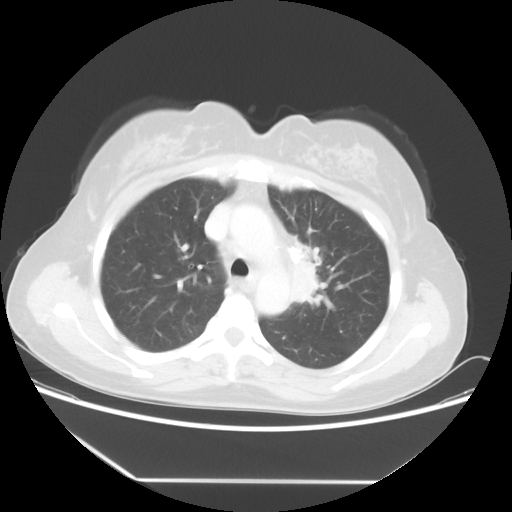
Chest CT, one axial slice; position 37 of 52 along the scan axis; 100 kVp; lung window (W 1500 / L -600 HU); 5 mm slice thickness; 512 × 512 image matrix. Female patient, age 50 years. Case-level facts recorded for this patient, not image findings: clinical TNM (as recorded): T2 N3 M0.
Structures marked on this image (bounding box drawn by a radiologist):
- lung tumour (recorded histology: adenocarcinoma): bounding box (x1, y1, x2, y2) in pixels: (282, 224, 335, 319)